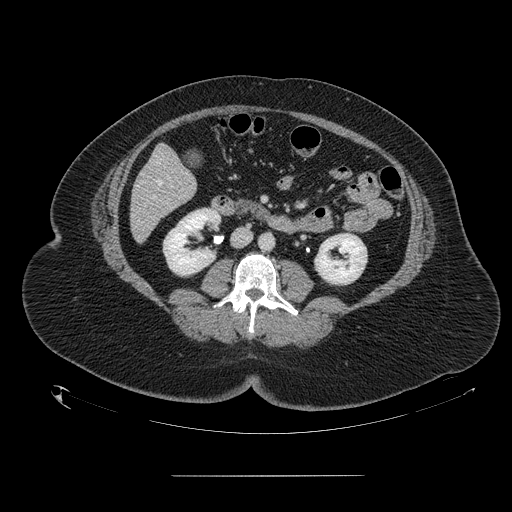
Contrast-enhanced abdominal CT, one axial slice. Slice 45 of 164 in the series (ordered by position). 120 kVp. Soft-tissue window (W 400 / L 40 HU). 512 × 512 image matrix, field of view 495 × 495 mm. Female patient, age 52 years. From the clinical record (not read from this slice): diagnosis: colorectal cancer liver metastases, imaged before liver resection; multiple liver metastases: yes; largest metastasis: 3.5 cm; disease in both lobes: no.
Outlined on this slice (outlined manually by an expert reader):
- hepatic veins: bounding box [x1, y1, x2, y2] px = [157, 162, 161, 185]
- liver: [131, 146, 196, 242]
- portal vein (with intrahepatic branches): [152, 196, 155, 198]